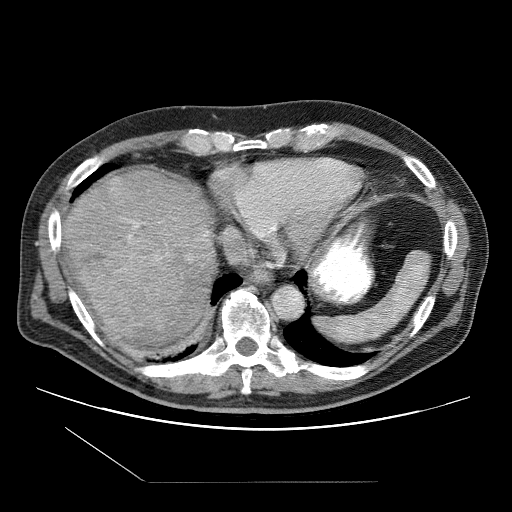
Contrast-enhanced abdominal CT (liver protocol), one axial slice; position 89 of 109 along the scan axis; reconstruction kernel STANDARD; one of 2 acquisitions stored at this slice position; soft-tissue window (W 400 / L 40 HU); 2.5 mm slice thickness; 512 × 512 image matrix, field of view 400 × 400 mm. Case-level facts recorded for this patient, not image findings: diagnosis: hepatocellular carcinoma (patient treated with transarterial chemoembolisation; whether this scan precedes or follows treatment is not stated here); TNM stage (as recorded): Stage-IIIB; Child-Pugh class: A; tumour differentiation: well differentiated; tumour nodularity: multinodular.
Structures marked on this image (semi-automatic segmentation, software-assisted and operator-edited):
- liver parenchyma outside the tumour (the mass and vessels are separate outlines, so this box may not span the whole liver): bounding box <62,170,216,344> (left, top, right, bottom; pixels)
- mass: <68,239,186,339>
- liver vessels: <128,222,206,238>